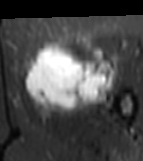
MRI of an extremity soft-tissue mass, one axial slice; position 29 of 81 along the scan axis; STIR; MR volume resampled by the dataset authors to the PET/CT grid (not the native acquisition matrix); 3.27 mm slice thickness; 143 × 161 image matrix, field of view 140 × 157 mm. Female patient. Case-level facts recorded for this patient, not image findings: histological type: myxofibrosarcoma; grade: intermediate; site of the primary tumour: left thigh.
Annotated regions visible in this slice (expert contour drawn on MRI and transferred to this co-registered scan by the dataset authors):
- gross tumour volume including surrounding oedema: bounding box [x1, y1, x2, y2] px = [24, 44, 118, 118]
- gross tumour volume (mass): [26, 44, 114, 109]